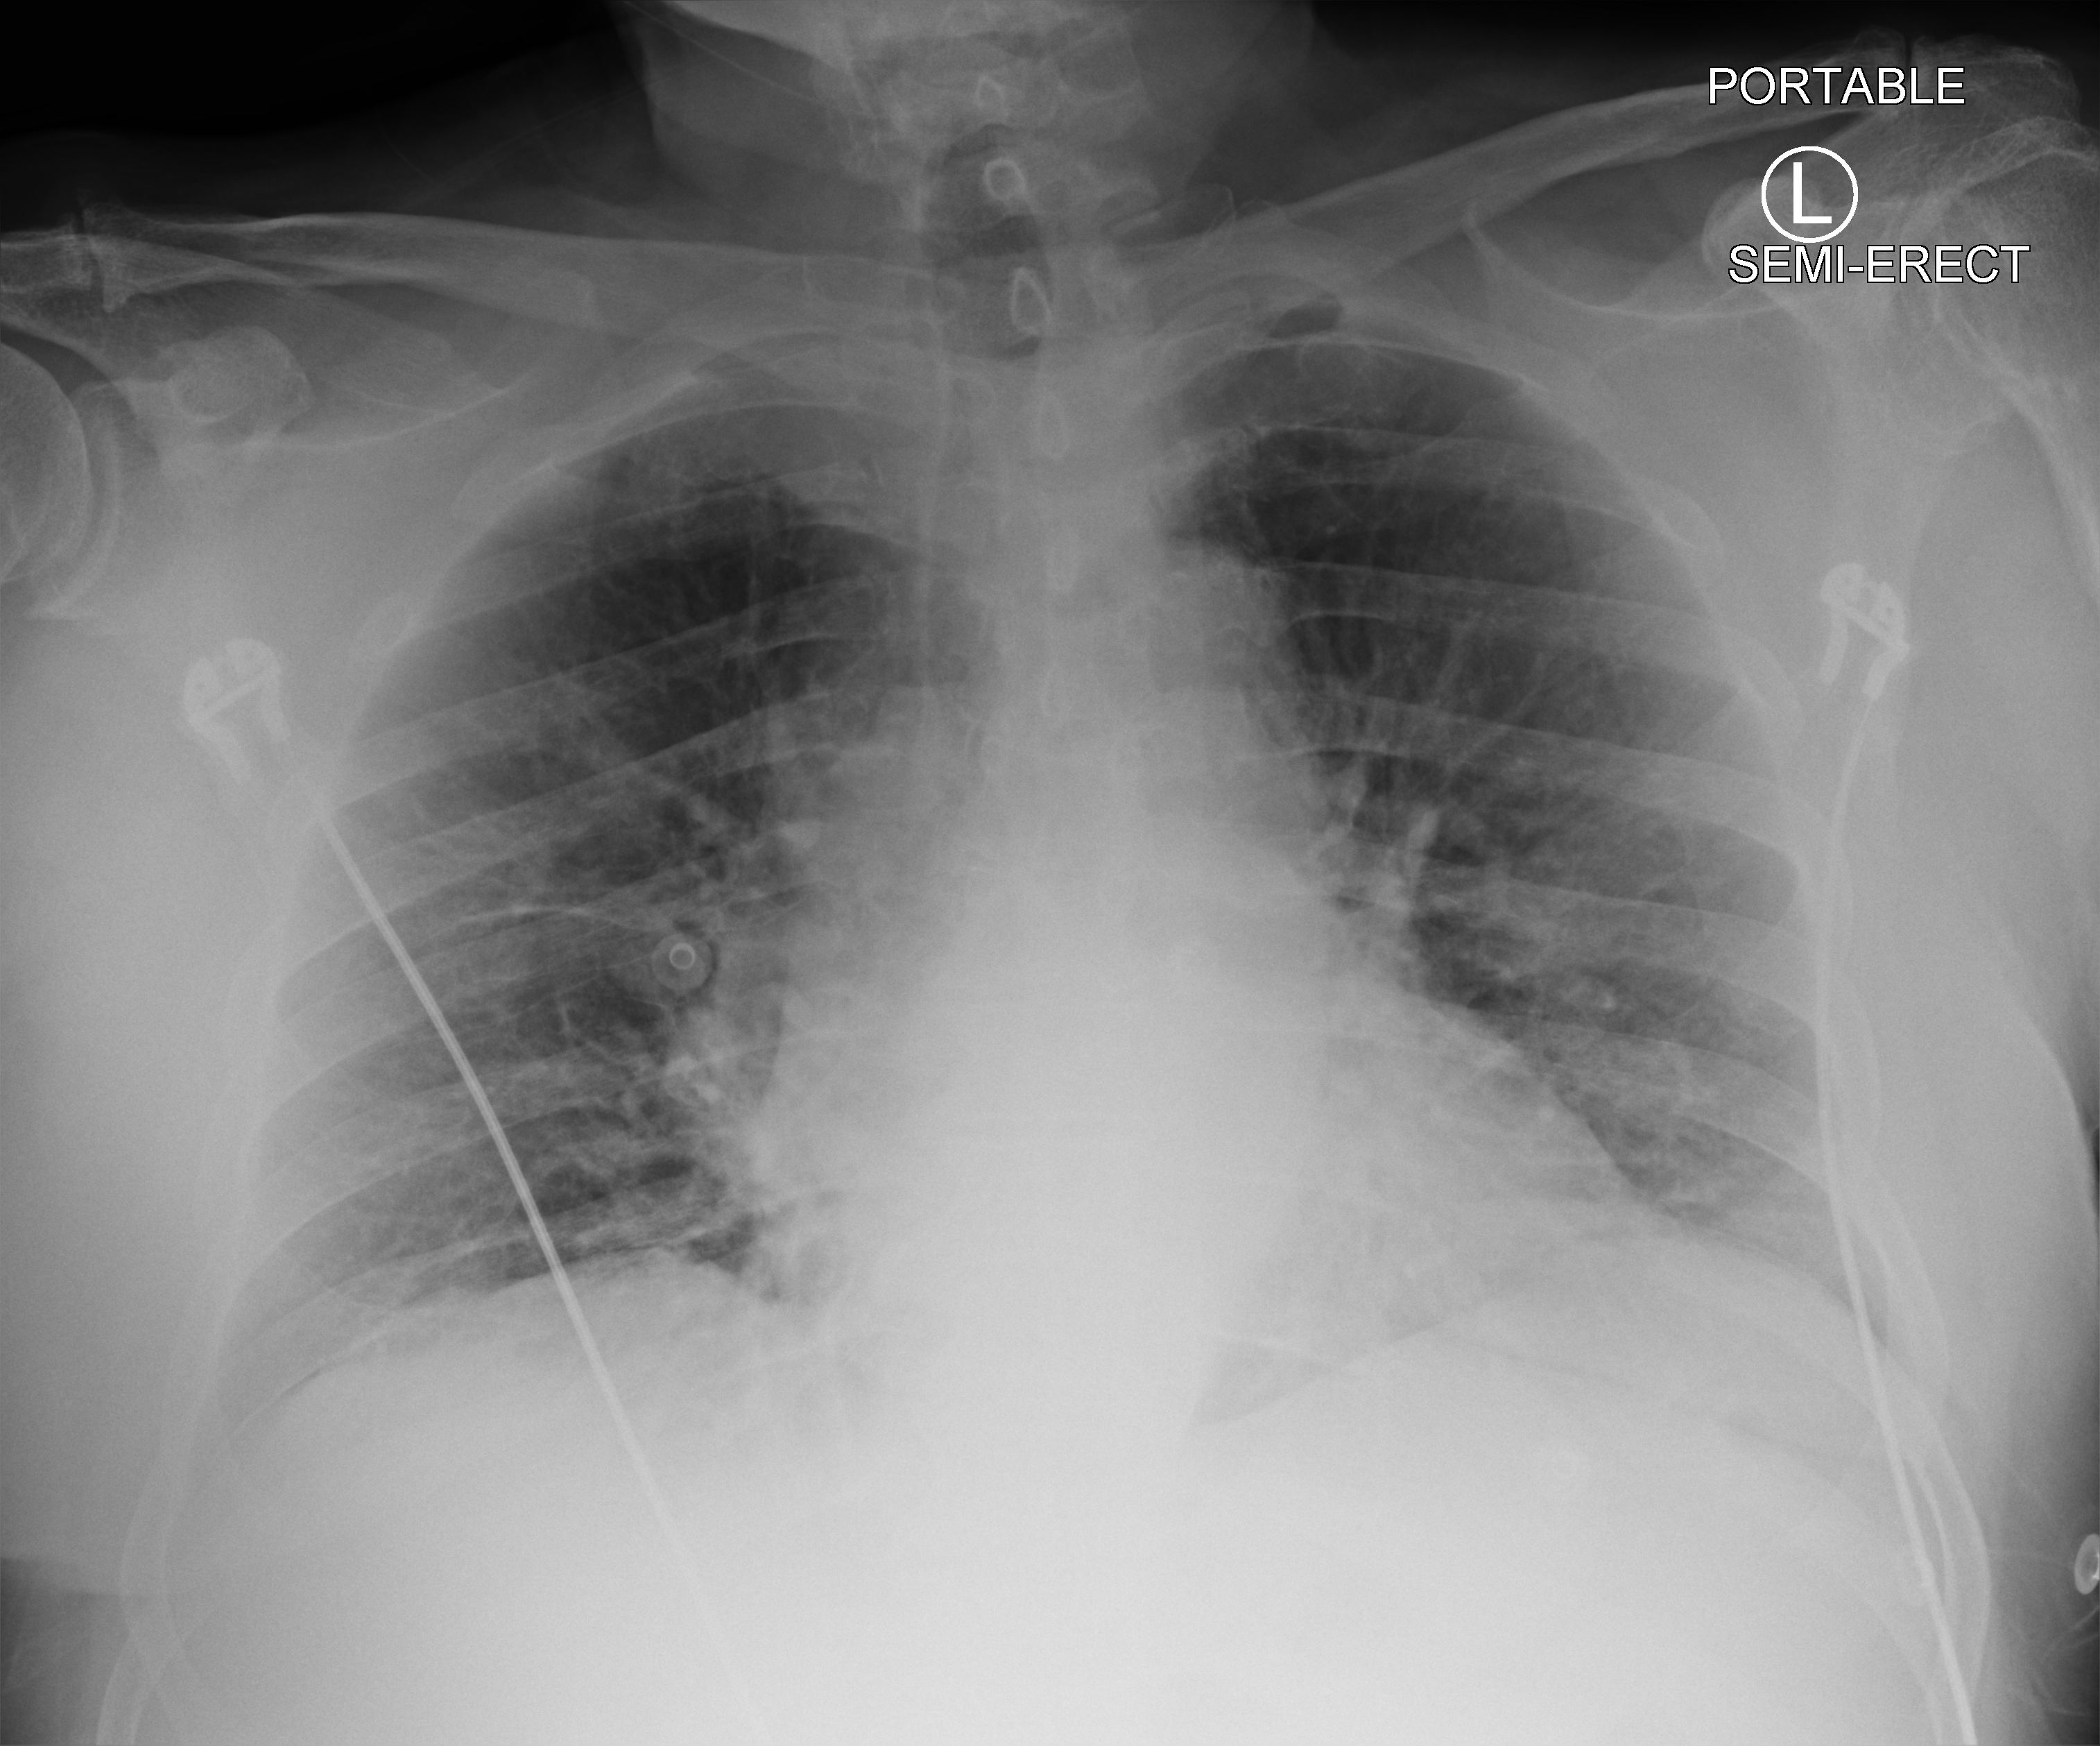
Chest X-ray (portable). Patient hospitalised with COVID-19; male, aged 60–74 years.
Admission-level facts for this patient (not findings on this image; timing relative to this image not recorded): length of hospital stay: 20 days.